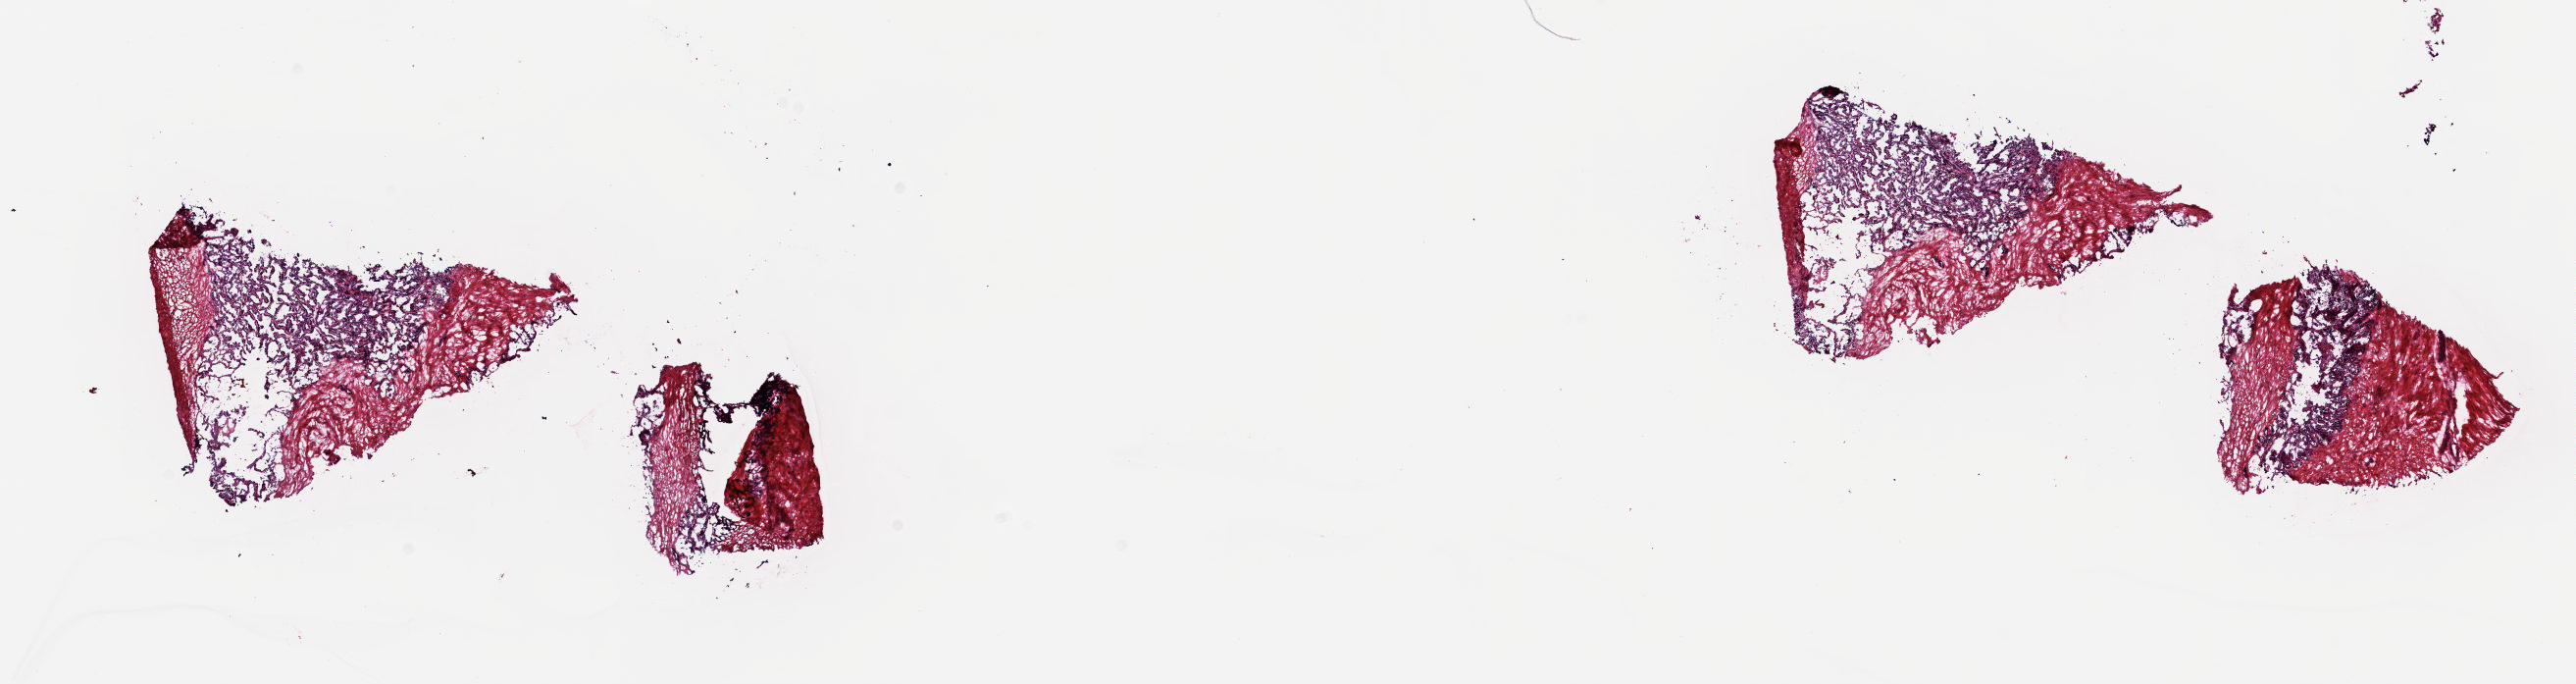
Whole-slide histology image, Hematoxylin and eosin (H&E) stained — whole scanned area (about 20.8 x 5.5 mm, slide scanned at 20x) shown as a low-resolution overview; frozen section from the top of the tissue portion; solid tissue normal (non-tumour tissue) sample from the prostate. Patient: male, age at initial diagnosis 65 years. Slide review estimates, as recorded: tumour cells 0%, tumour nuclei 0%, normal cells 50%, stromal cells 50%, necrosis 0%. Inflammatory infiltration, as recorded: lymphocyte infiltration 3%, monocyte infiltration 0%, neutrophil infiltration 0%.
- this section: solid tissue normal (non-tumour) sample from the same patient
- patient diagnosis: Adenocarcinoma, NOS (prostate gland)